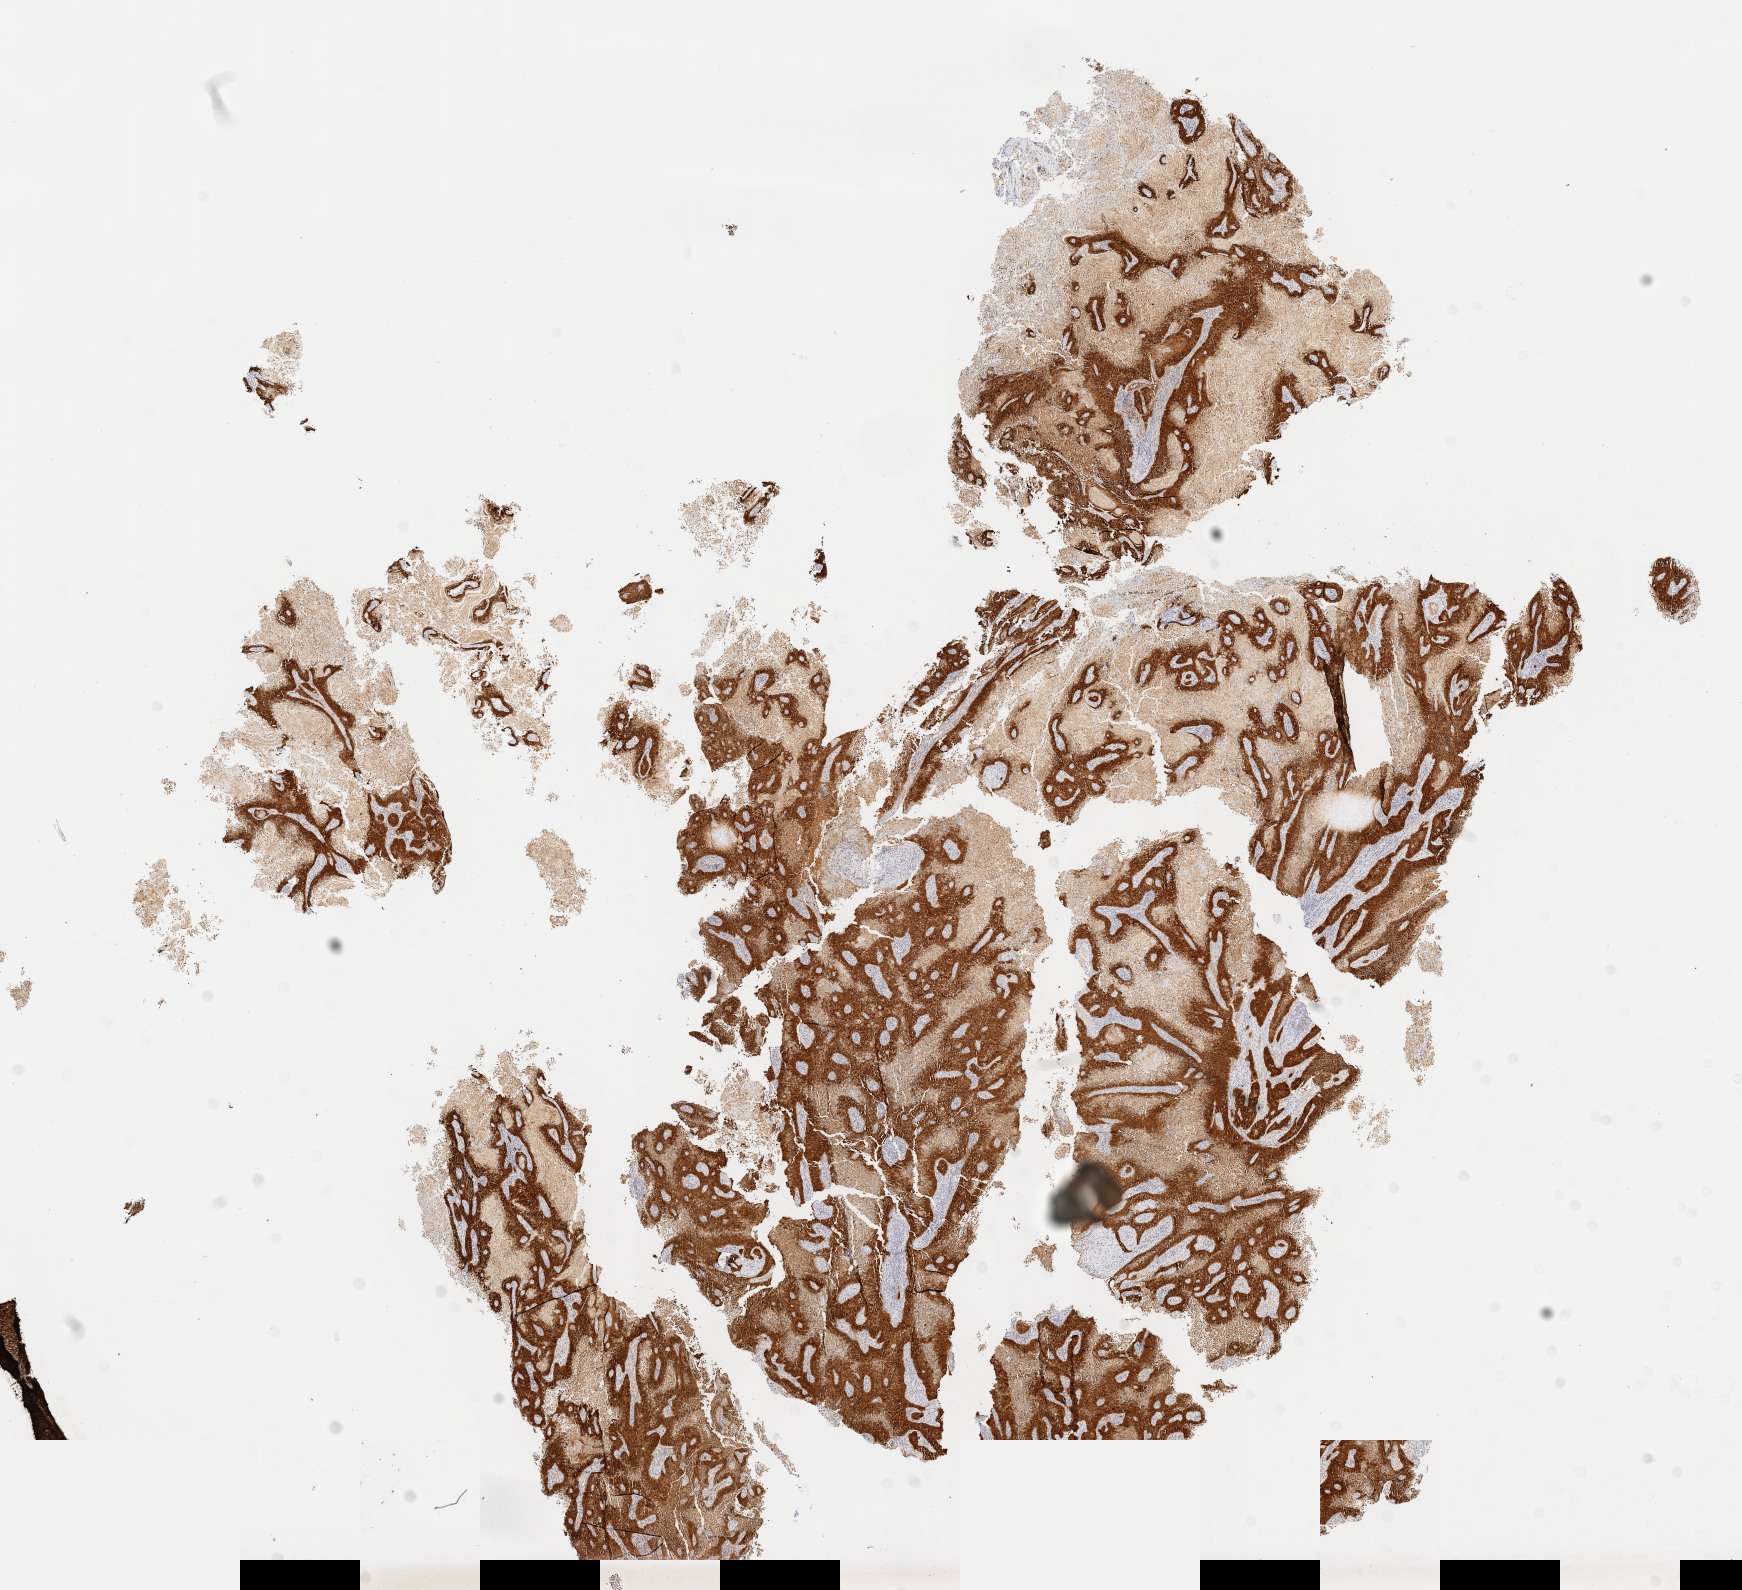
Whole-slide image, immunohistochemical stain for p16 (p16INK4a), whole scanned area (about 14.1 x 12.9 mm) shown as a low-resolution overview; specimen: tumor tissue; site: cervix. Patient: female, aged 42.
Histologic diagnosis: Squamous cell carcinoma, keratinizing, NOS.